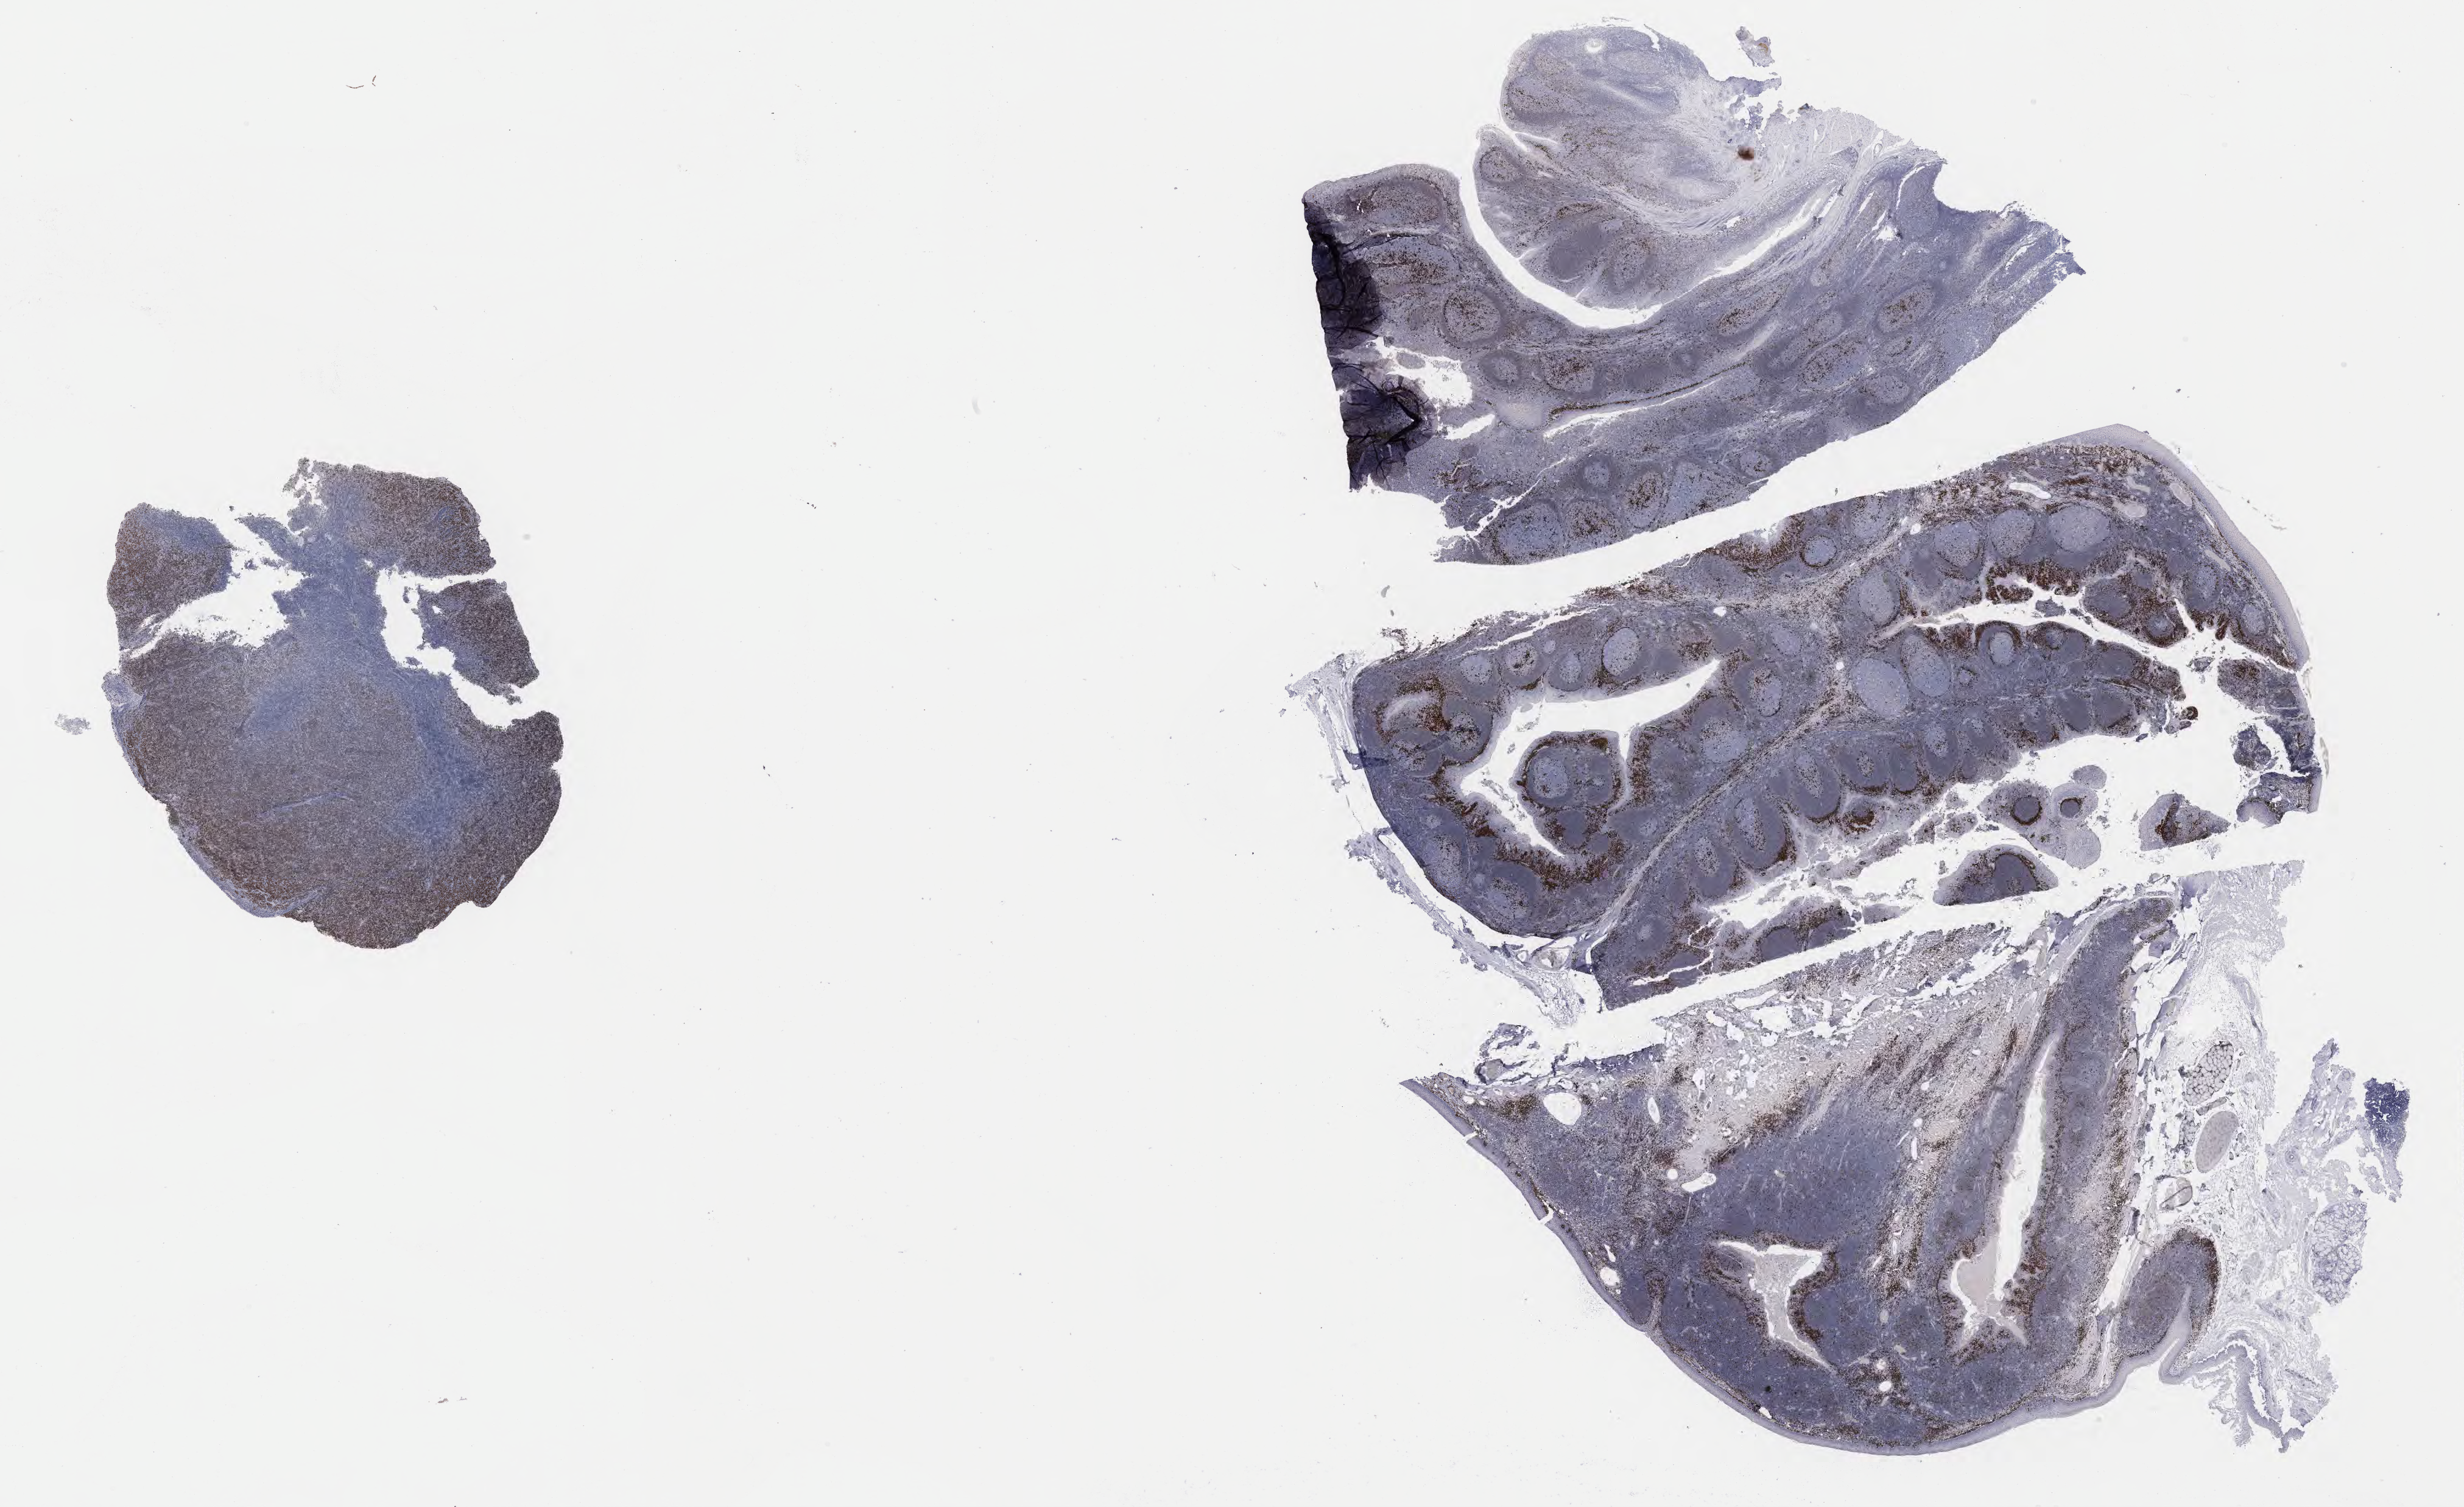
Immunohistochemistry (IHC) whole-slide image stained for IRF4/MUM1 — shown as a low-resolution overview of the whole scanned area (about 32.7 x 20.0 mm); tumor tissue; anatomic site: liver. Patient male; aged 46.
* diagnosis: Diffuse large B-cell lymphoma, NOS